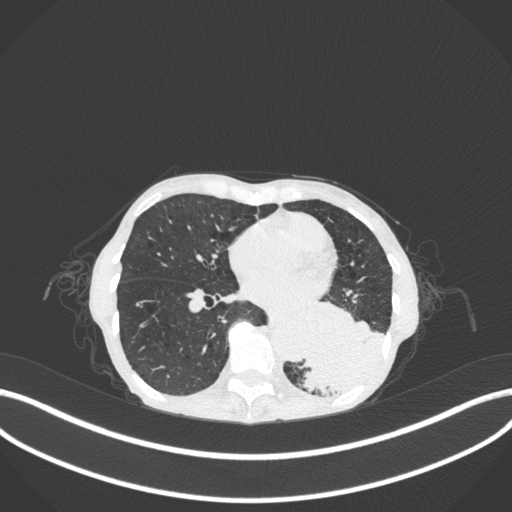
Chest CT, one axial slice. Slice 109 of 347 in the series (ordered by position). Reconstruction kernel B31f. 120 kVp. Lung window (W 1500 / L -600 HU). 1 mm slice thickness. 512 × 512 image matrix, field of view 400 × 400 mm. Female patient, age 70 years. Case-level facts recorded for this patient, not image findings: clinical TNM (as recorded): T3 N0 M0.
Outlined on this slice (bounding box drawn by a radiologist):
- lung tumour (recorded histology: small cell carcinoma): bounding box <296,289,391,397> (left, top, right, bottom; pixels)